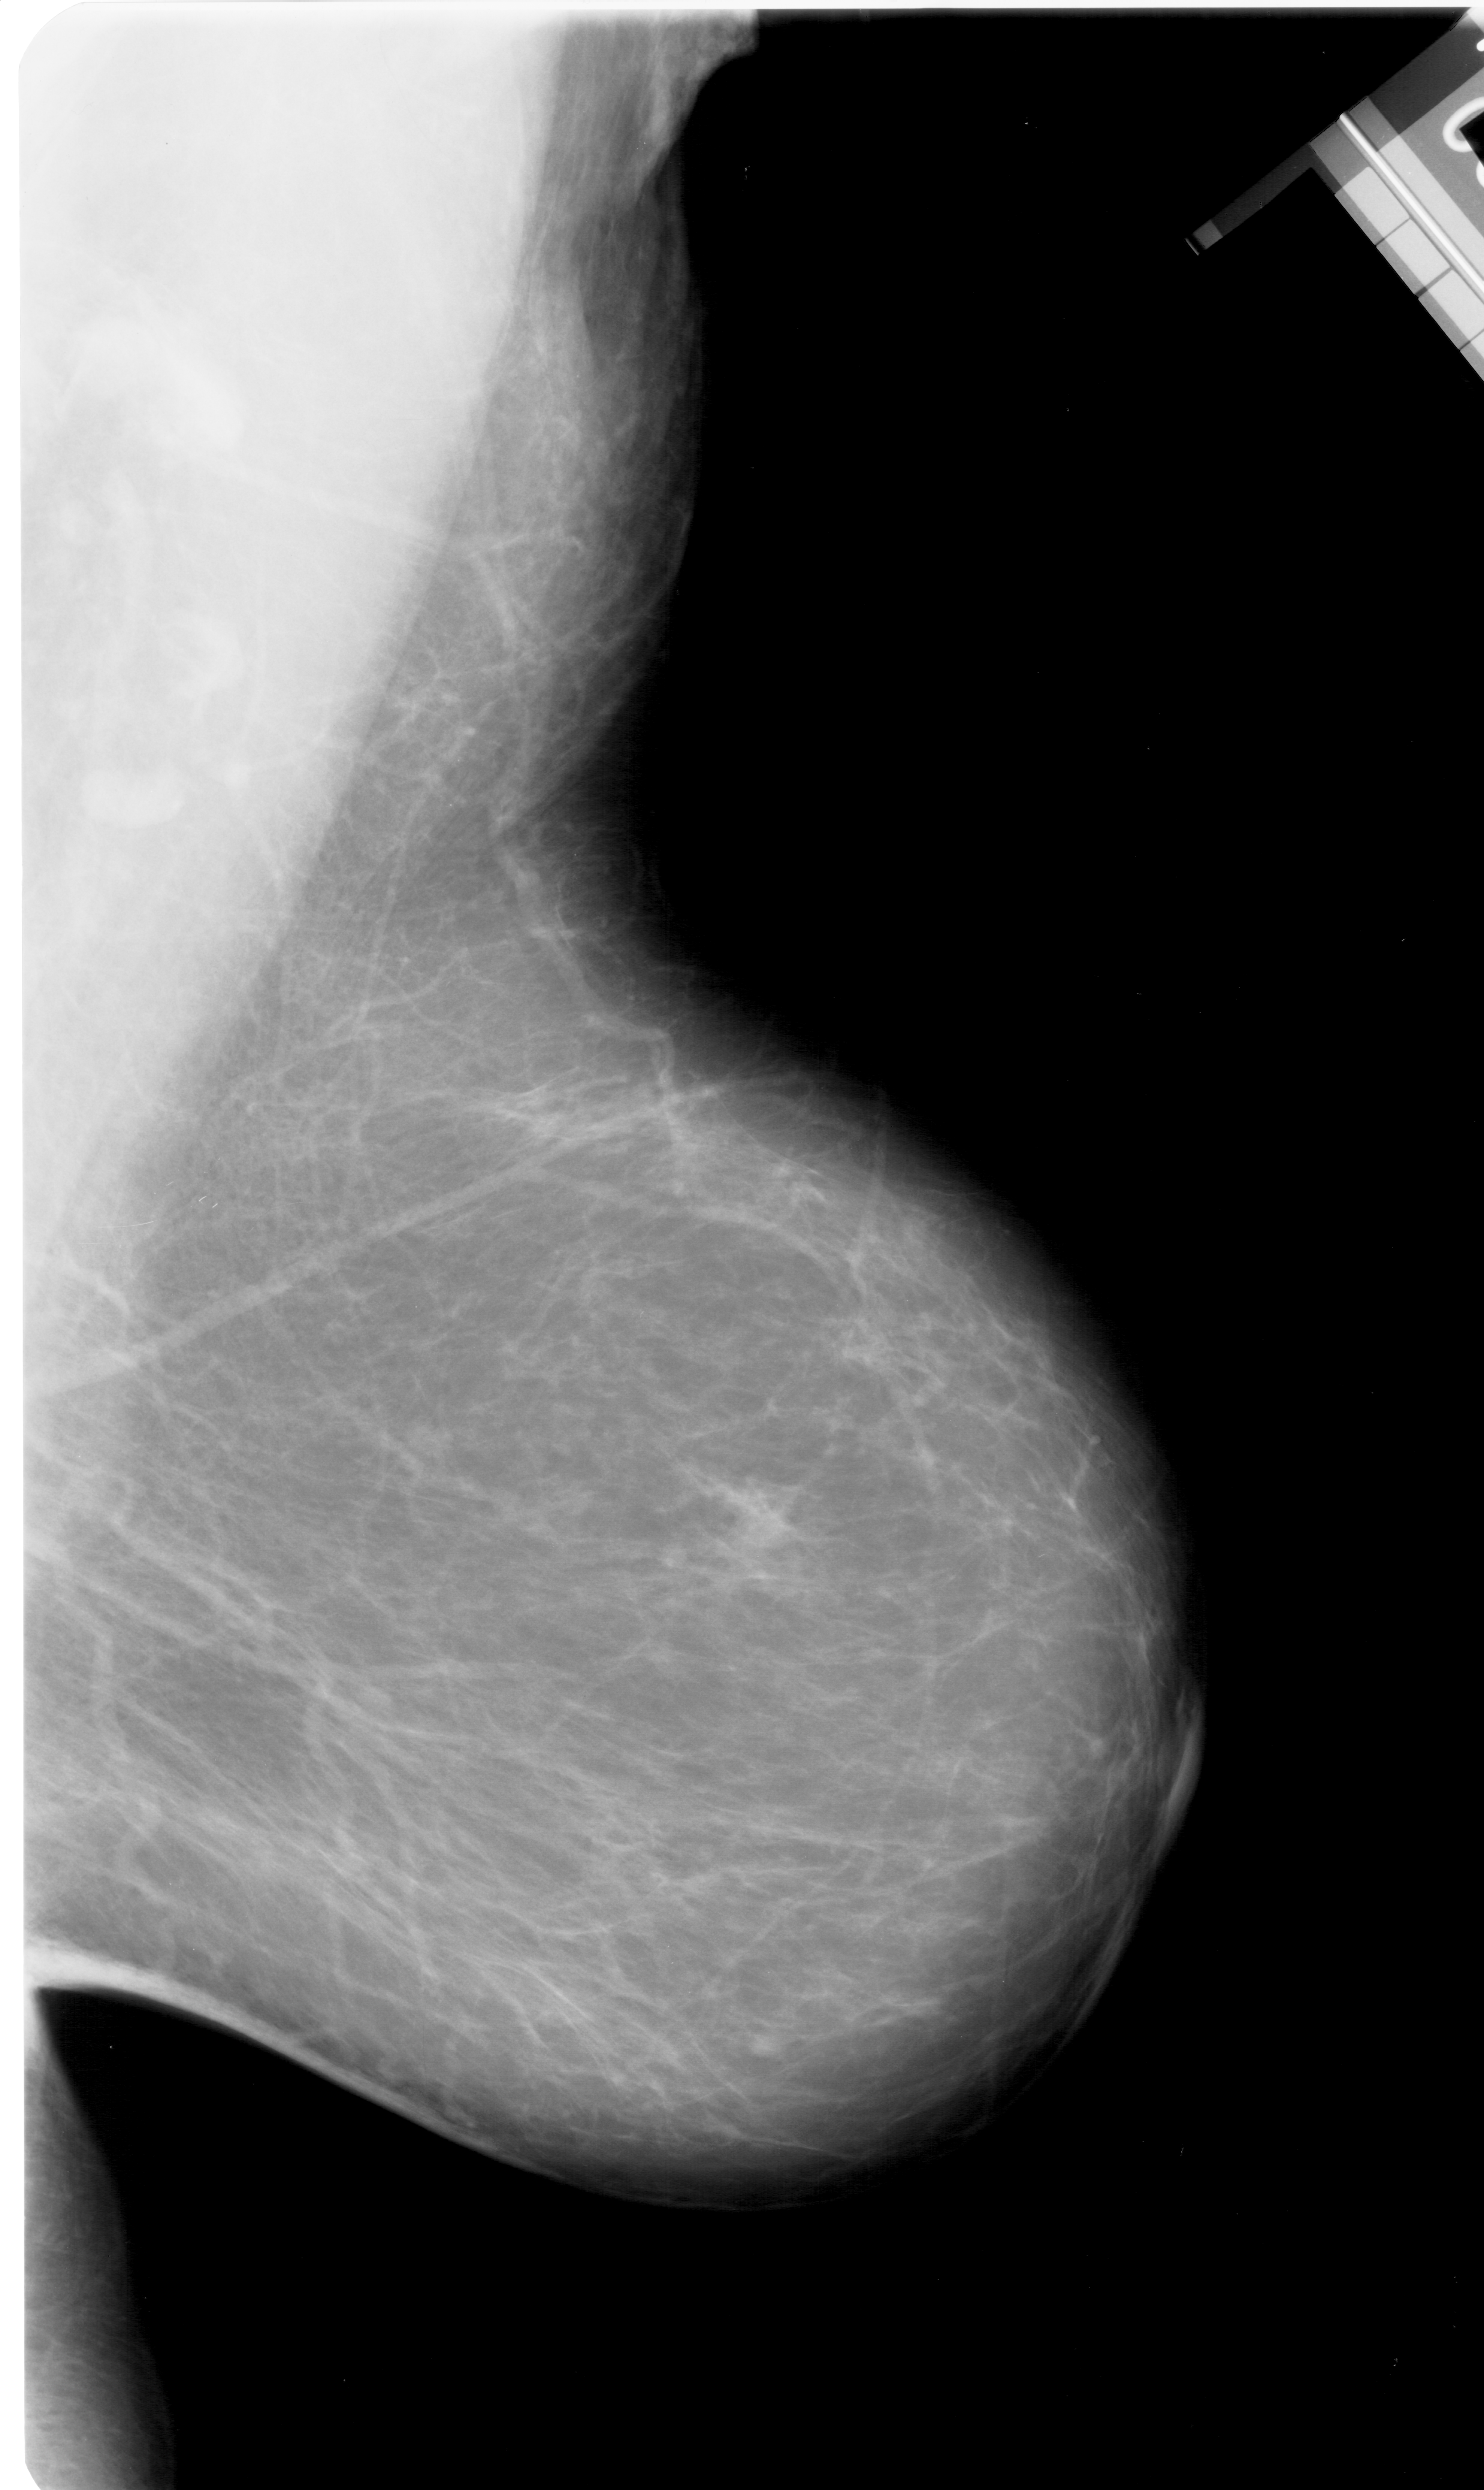
Digitized screen-film mammogram, right breast, mediolateral oblique (MLO) view, breast composition: scattered fibroglandular densities (BI-RADS density category 2 of 4).
- Abnormality record for this image: mass, shape lobulated, margins circumscribed; BI-RADS assessment category 4; pathology (as recorded): malignant.